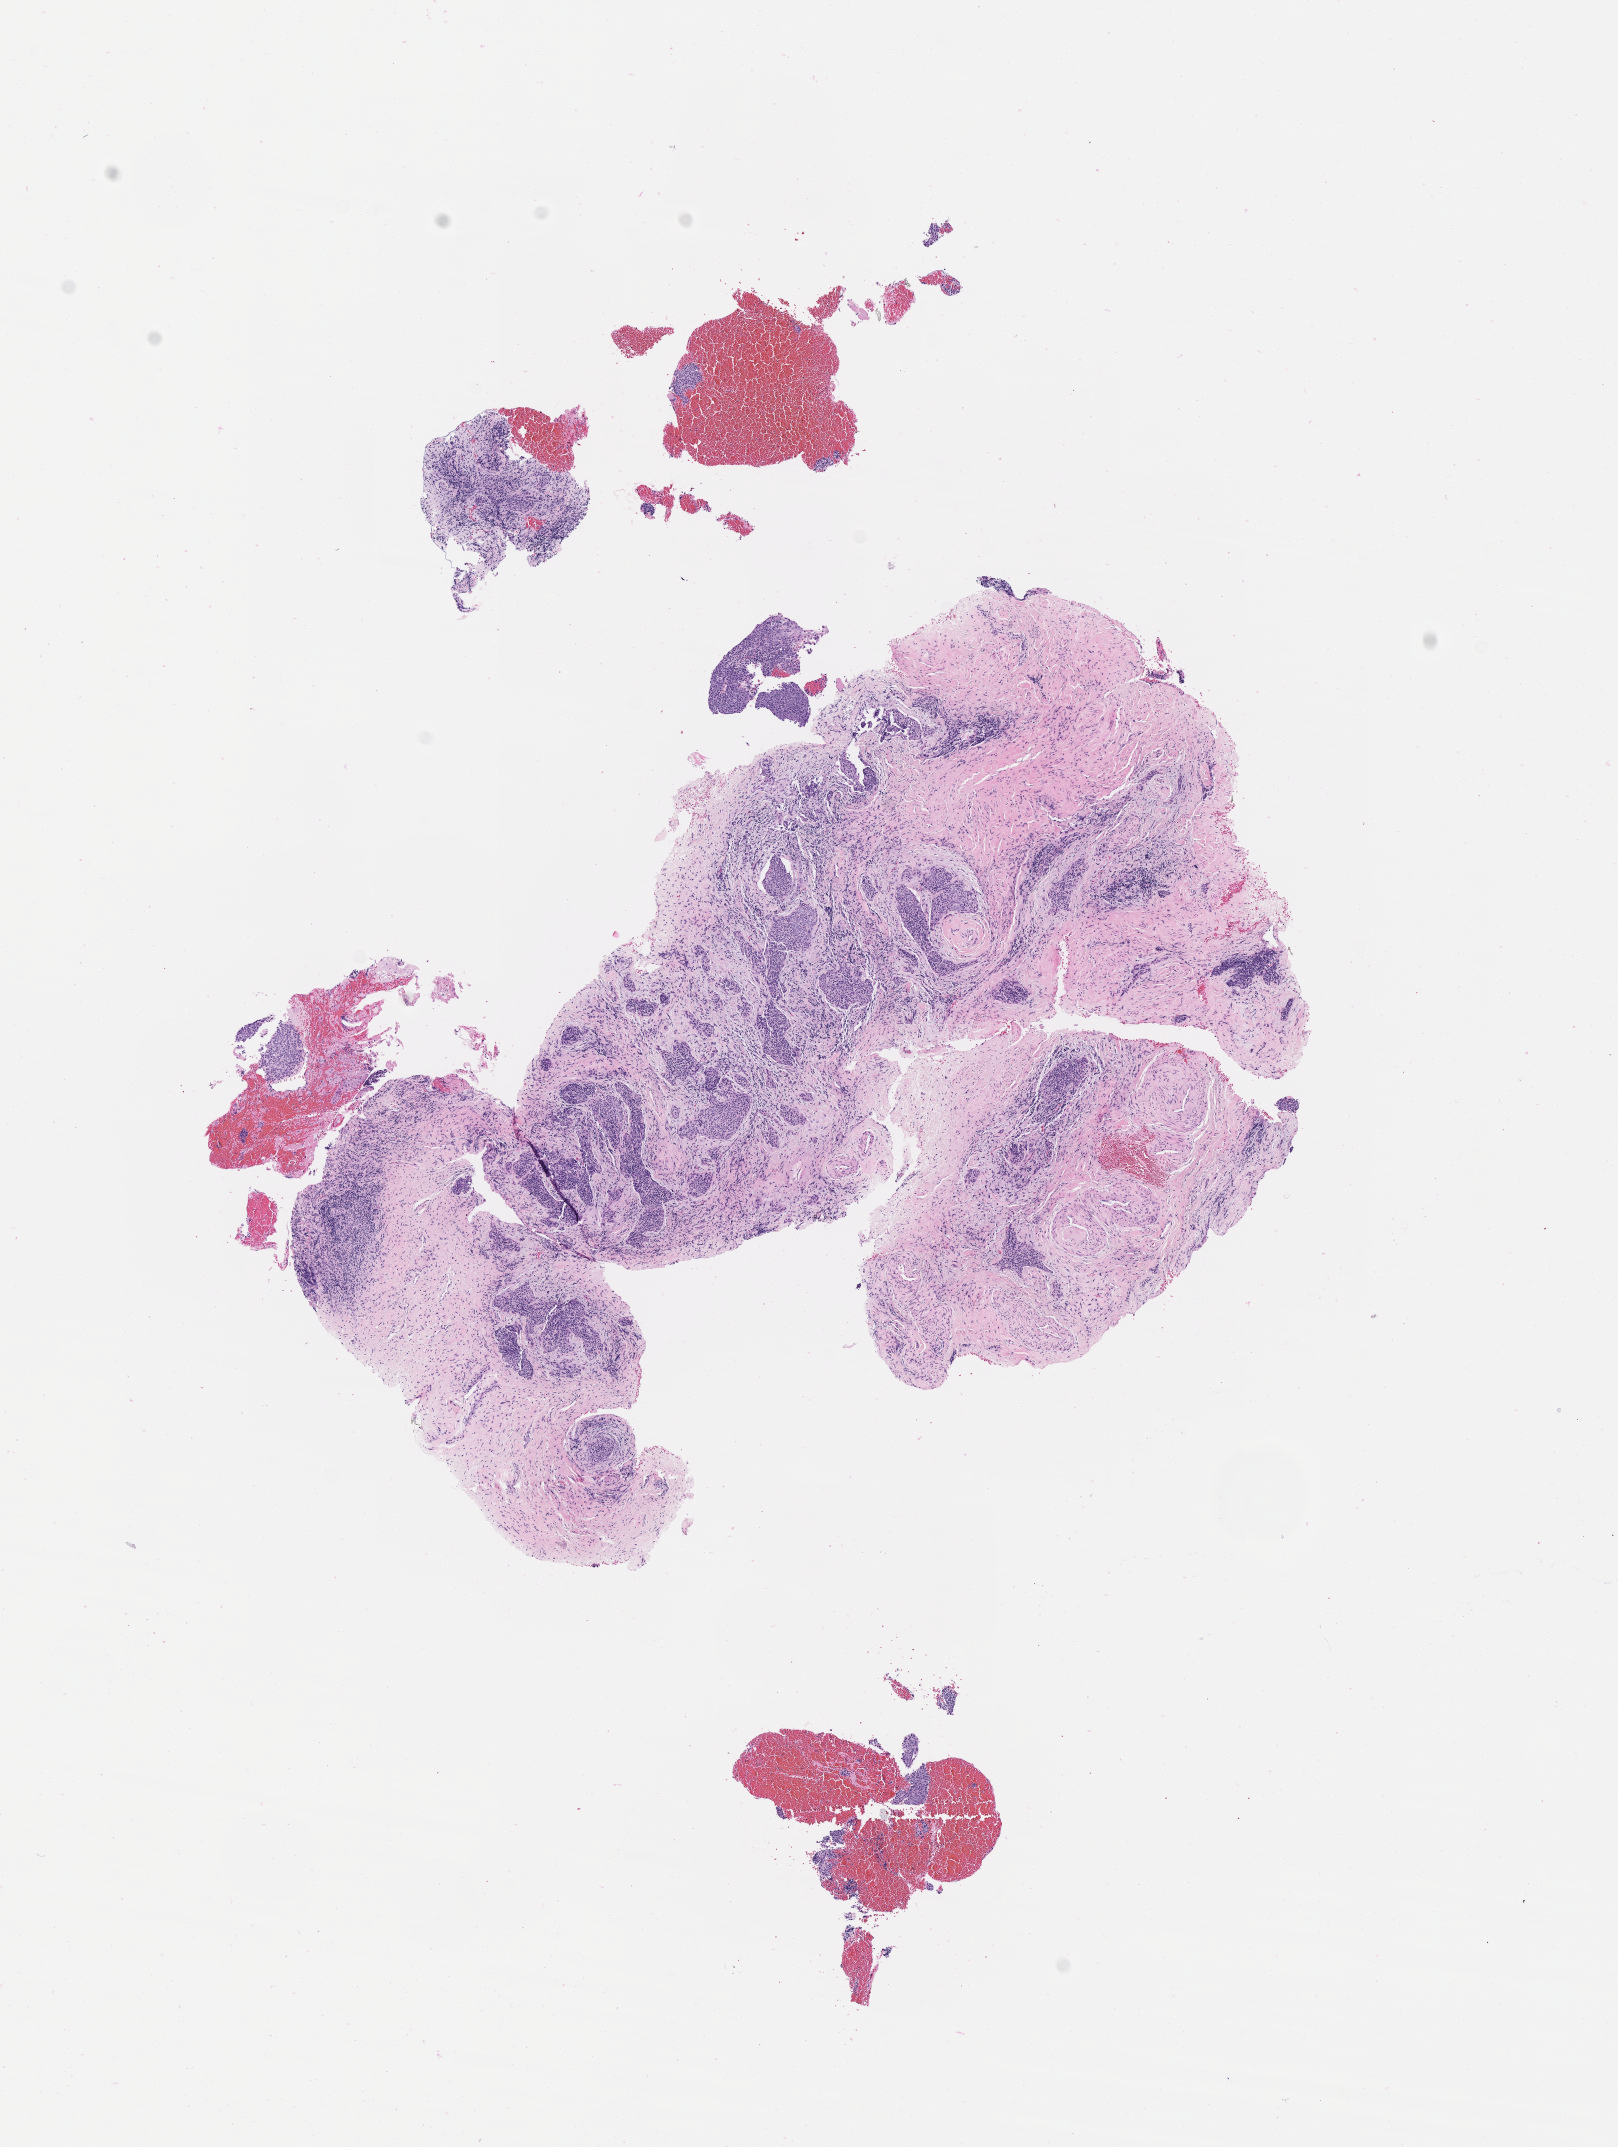
Hematoxylin and eosin (H&E) whole-slide image — low-resolution overview of the scanned area, about 6.5 x 8.7 mm, tumor tissue, site: cervix. Patient female; aged 58.
Diagnosis: Squamous cell carcinoma, large cell, nonkeratinizing, NOS.